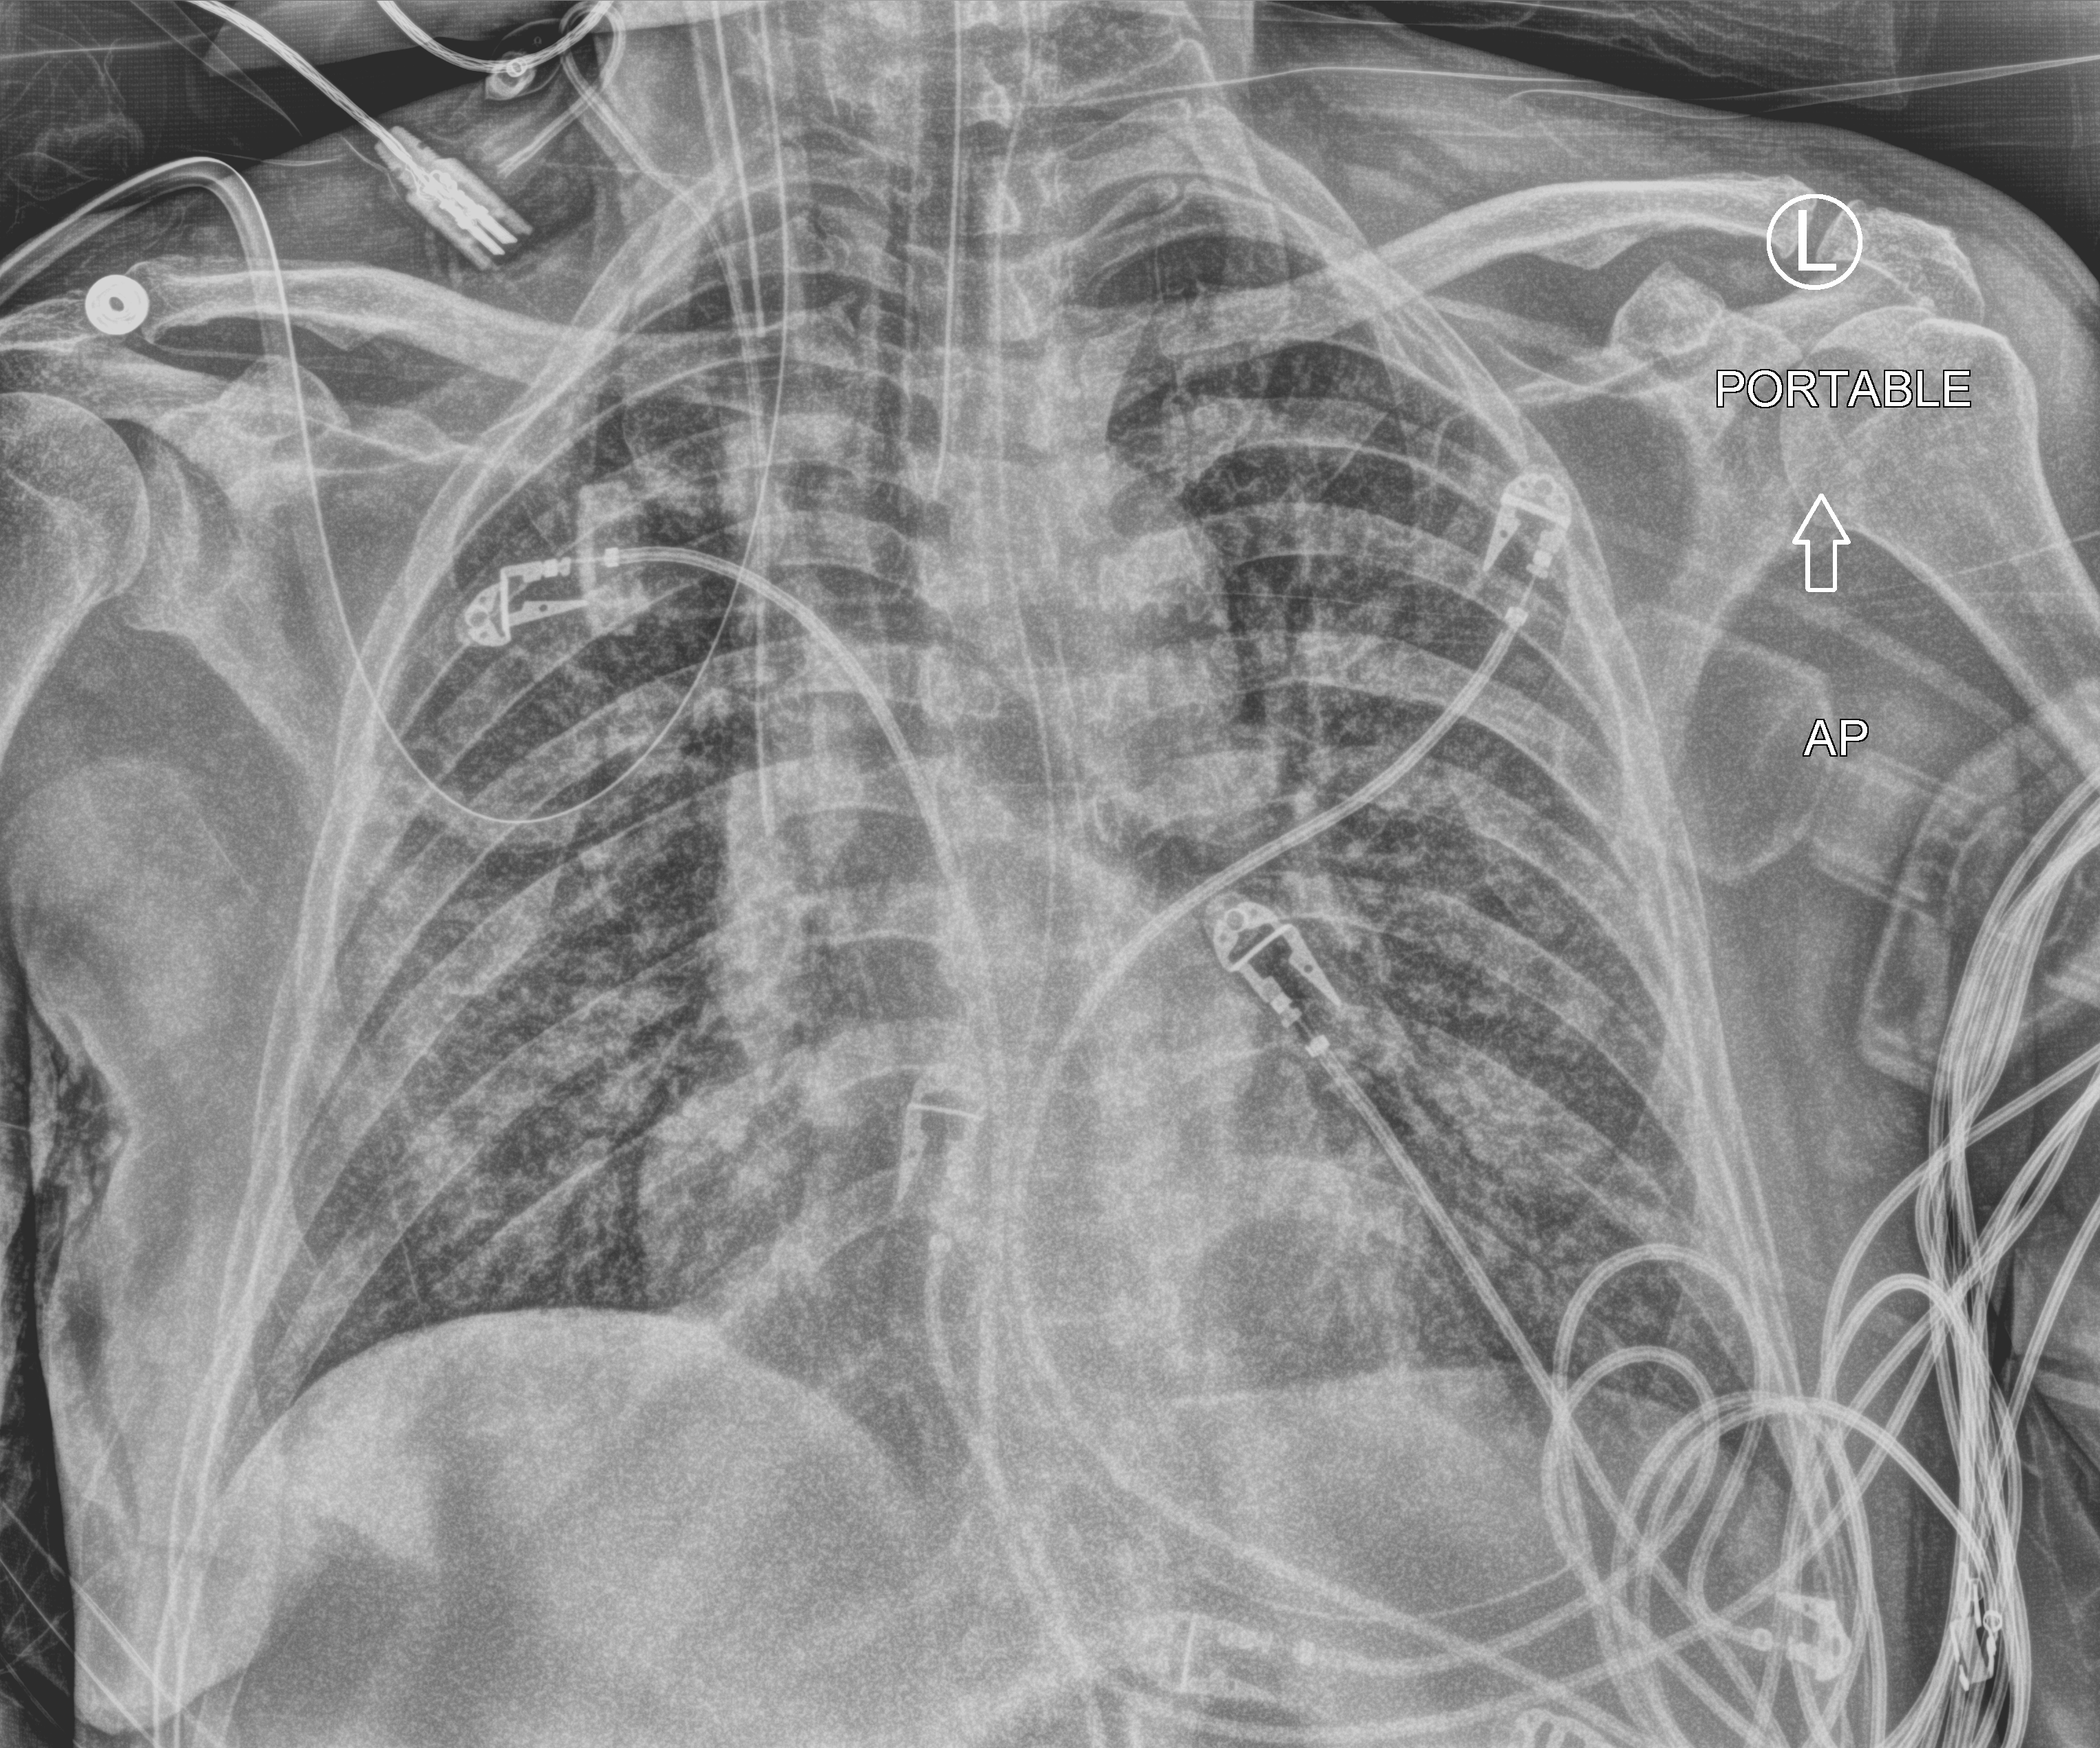
Chest X-ray (portable); anteroposterior (AP) projection. Male patient hospitalised with COVID-19, age 60–74 years.
Admission-level facts for this patient (not findings on this image; timing relative to this image not recorded): mechanically ventilated during this hospital stay: yes.